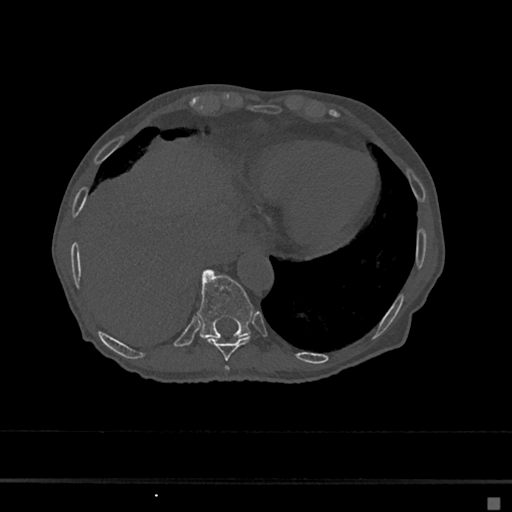
CT including the spine, one axial slice; slice 247 of 797 in the series (ordered by position); 120 kVp; bone window (W 1800 / L 400 HU); 0.5 mm slice thickness; 512 × 512 image matrix, field of view 360 × 360 mm. Female patient, age 68 years. Case-level facts recorded for this patient, not image findings: primary cancer: renal.
Annotated regions visible in this slice (semi-automatic segmentation, software-assisted and operator-edited):
- T10 vertebra: bounding box <197,270,253,339> (left, top, right, bottom; pixels)
- T8 vertebra: <224,367,229,371>
- T9 vertebra: <207,337,251,361>